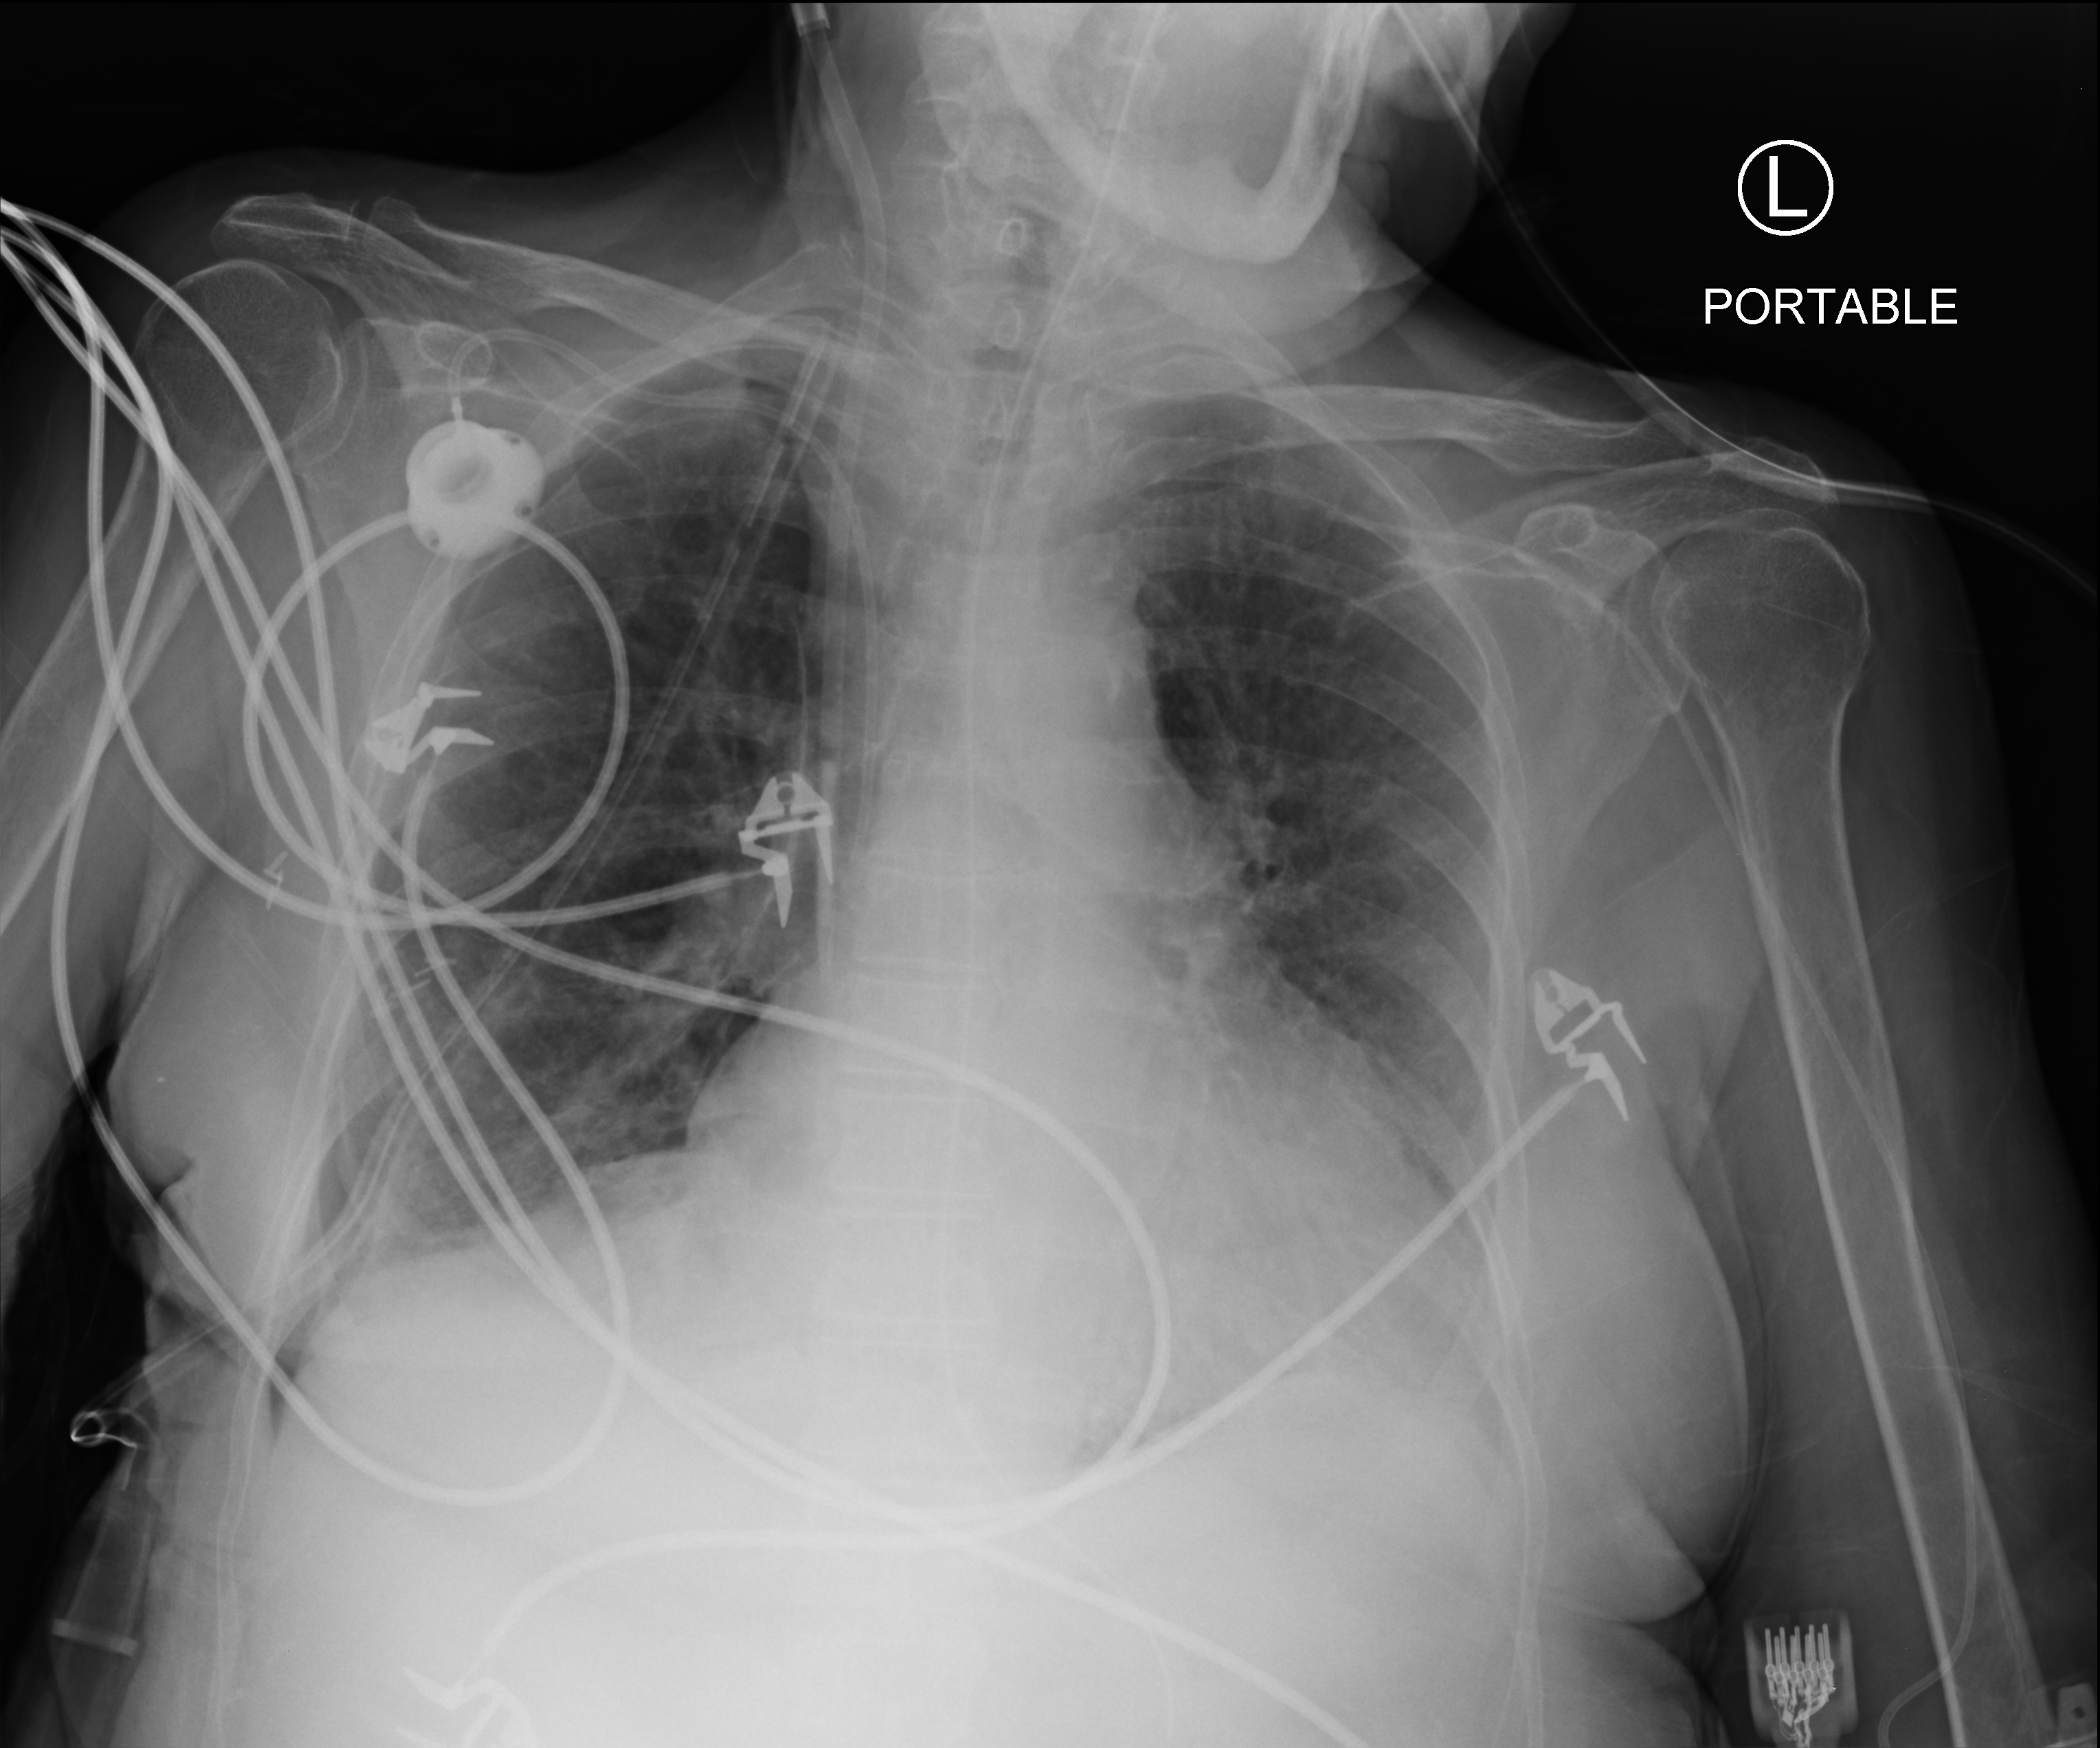
Portable chest radiograph. Female patient hospitalised with COVID-19, age 60–74 years.
Admission-level facts for this patient (not findings on this image; timing relative to this image not recorded): mechanically ventilated during this hospital stay: yes.